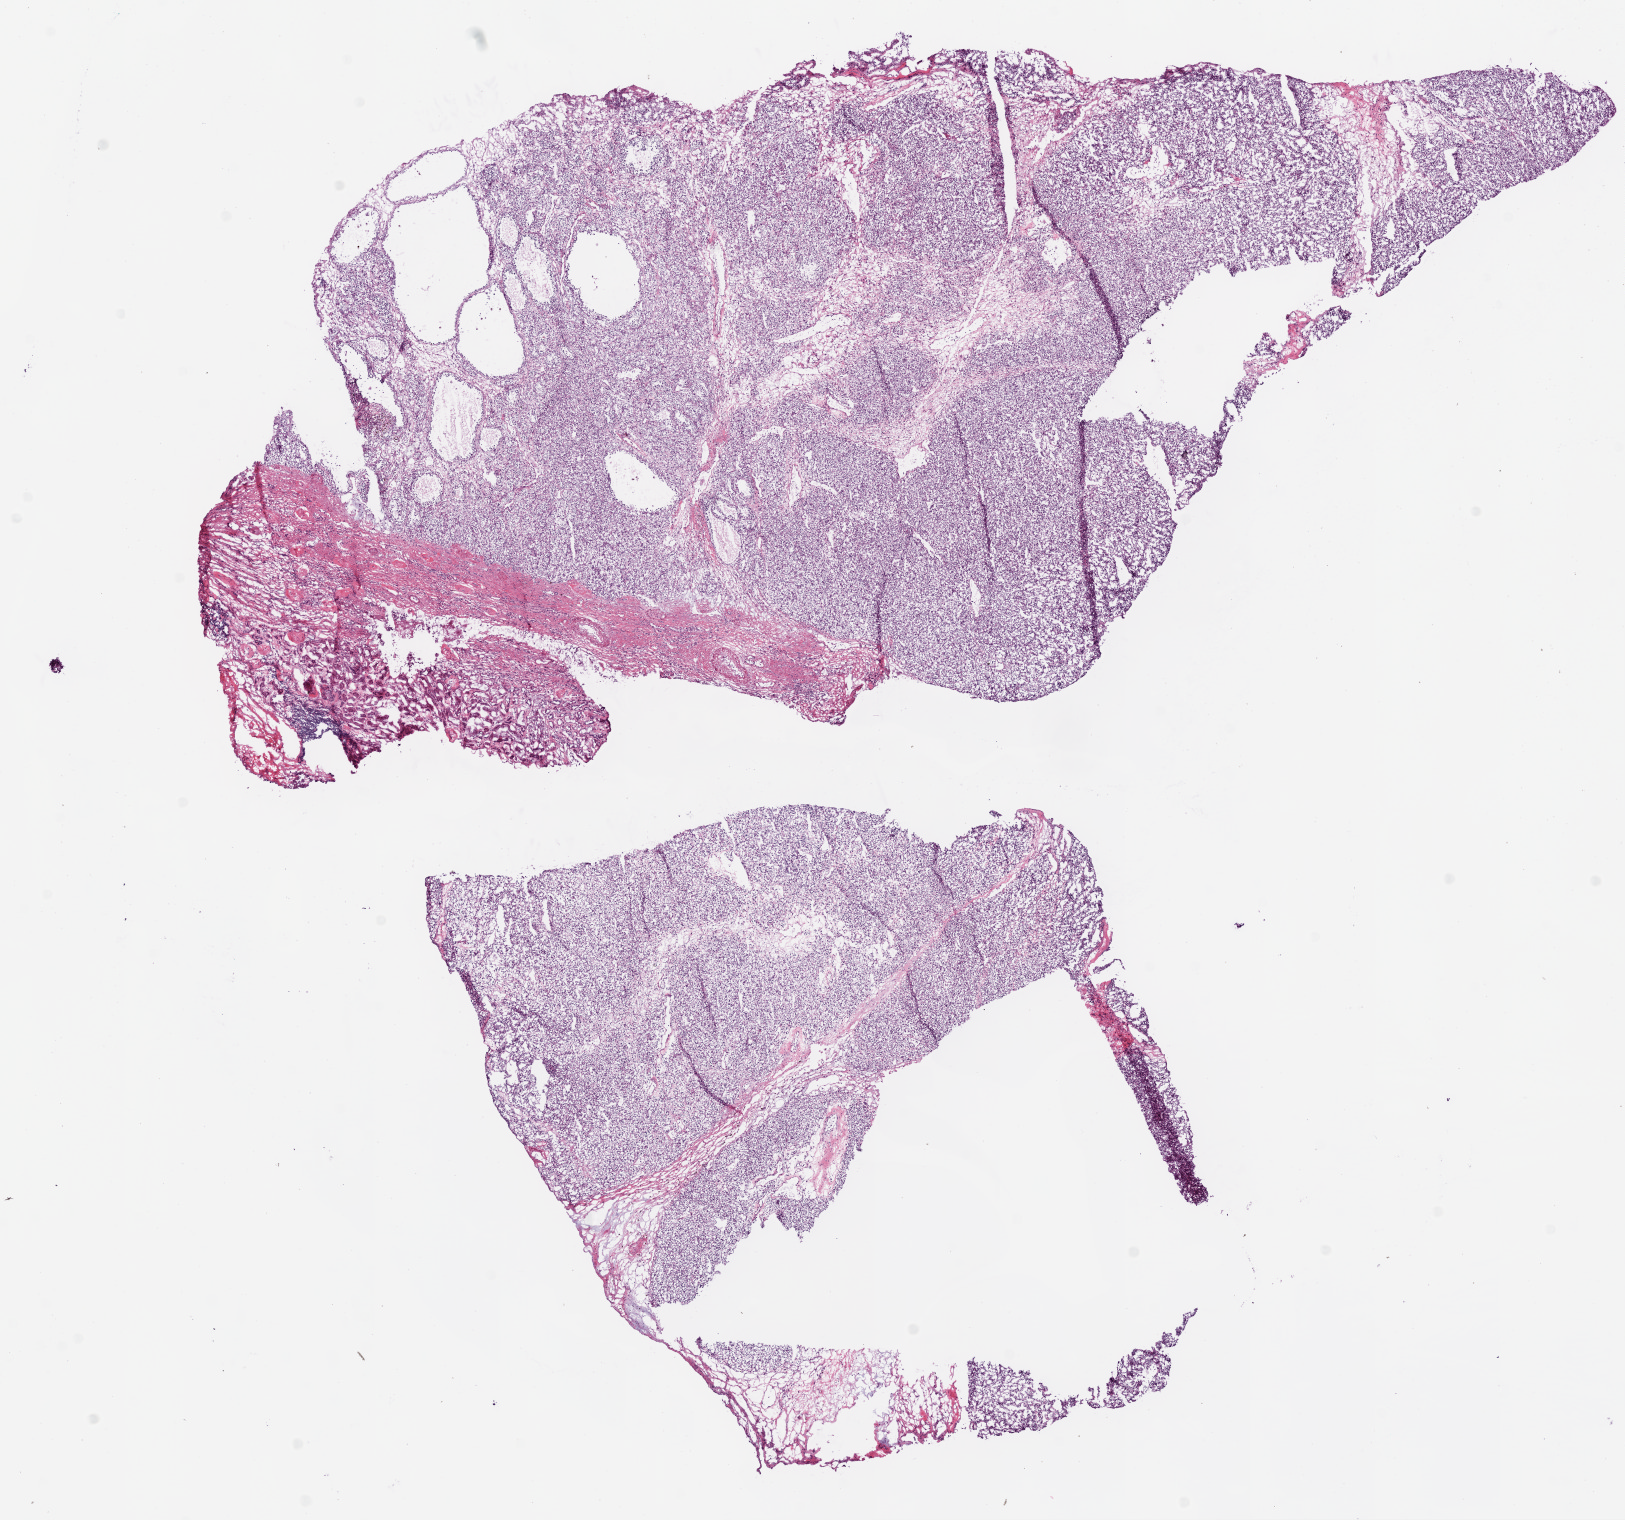
Digitized H&E-stained tissue section (whole slide), a low-resolution overview of the entire scanned area, about 13.0 x 12.2 mm (acquisition: 20x scan), frozen section, primary tumour sample from the kidney. Patient: male, age at initial diagnosis 72 years.
Histologic diagnosis: Clear cell adenocarcinoma, NOS.